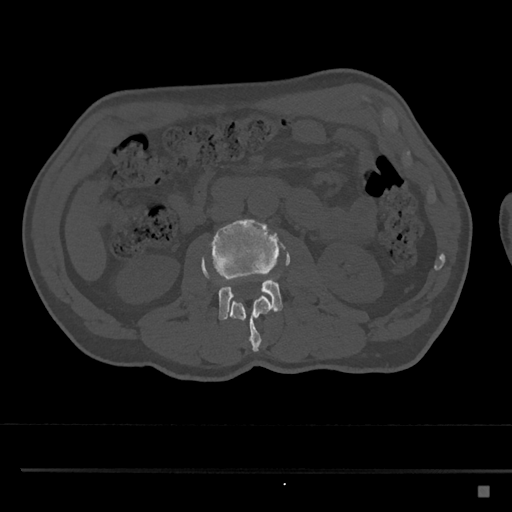
CT including the spine, one axial slice. Position 725 of 797 along the scan axis. Reconstruction kernel Br40s/3. 120 kVp. Bone window (W 1800 / L 400 HU). 0.5 mm slice thickness. 512 × 512 image matrix, field of view 391 × 391 mm. Patient: male, 59 years. From the clinical record (not read from this slice): primary cancer: prostate.
Outlined on this slice (semi-automatic segmentation, software-assisted and operator-edited):
- L2 vertebra: bounding box (x1, y1, x2, y2) in pixels: (202, 259, 273, 352)
- L3 vertebra: (201, 219, 291, 320)